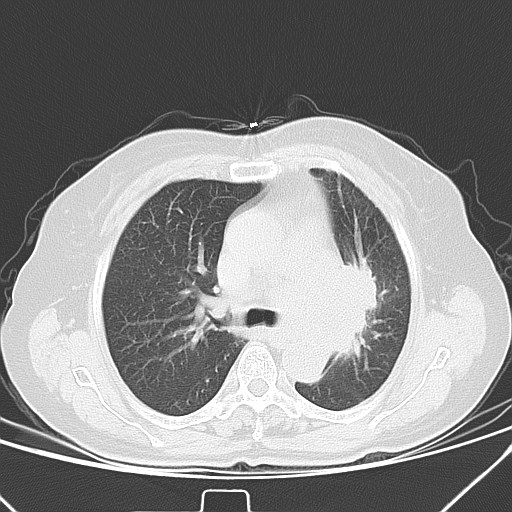
Chest CT, one axial slice. Slice 26 of 40 in the series (ordered by position). 120 kVp. Lung window (W 1500 / L -600 HU). 512 × 512 image matrix, field of view 331 × 331 mm. Patient: female, 59 years. Case-level facts recorded for this patient, not image findings: clinical TNM (as recorded): T3 N1 M0; histopathological grade: G3.
Outlined on this slice (rectangle marked by the reading radiologist):
- lung tumour (recorded histology: small cell carcinoma): bounding box [x1, y1, x2, y2] px = [340, 244, 387, 368]